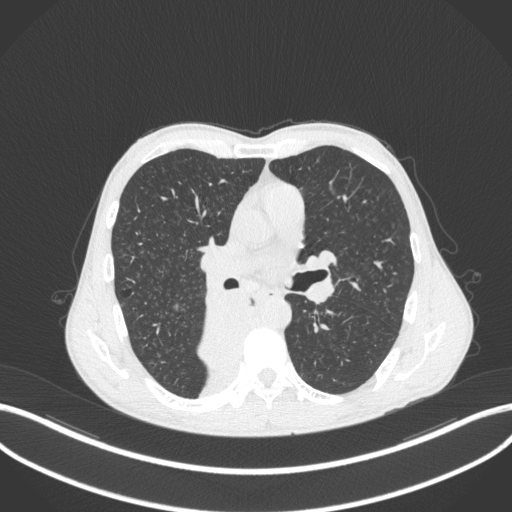
Chest CT, one axial slice. Slice 214 of 371 in the series (ordered by position). Reconstruction kernel B31f. 120 kVp. Lung window (W 1500 / L -600 HU). 1 mm slice thickness. 512 × 512 image matrix, field of view 400 × 400 mm. Male patient, age 58 years. From the clinical record (not read from this slice): clinical TNM (as recorded): T3 N1 M1.
Structures marked on this image (rectangle marked by the reading radiologist):
- lung tumour (recorded histology: squamous cell carcinoma): bounding box [x1, y1, x2, y2] px = [194, 285, 252, 378]